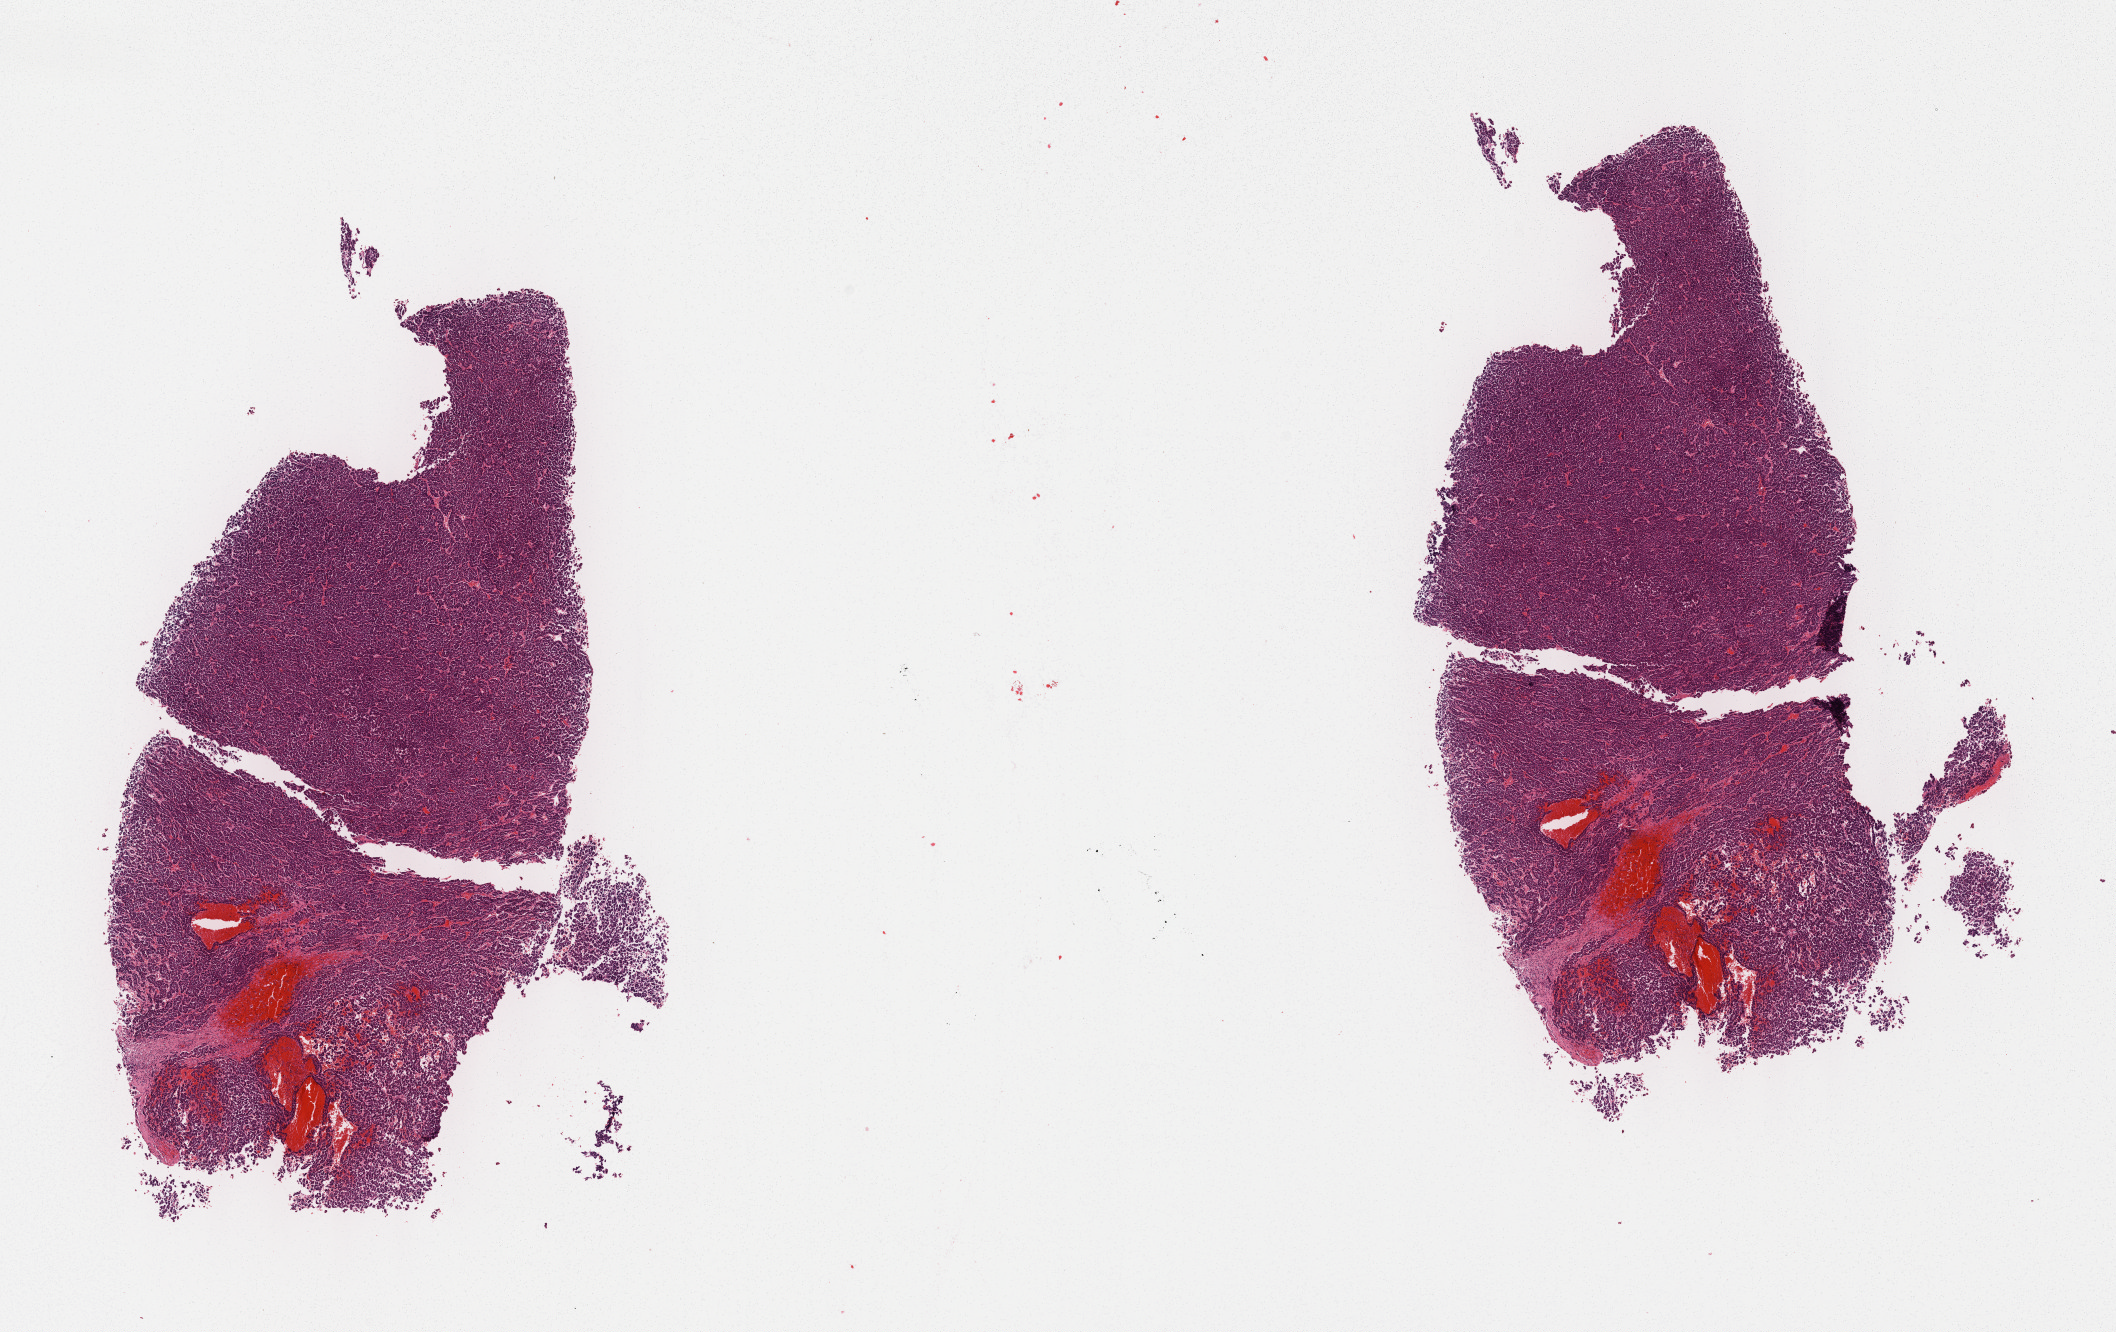
Whole-slide histology image, H&E, a low-resolution overview of the entire scanned area, about 17.1 x 10.8 mm (from a 40x scan); formalin-fixed paraffin-embedded (FFPE) diagnostic section; sample: primary tumour, liver. Patient: male, age at initial diagnosis 50 years. Histologic grade: G3 (poorly differentiated).
AJCC pathologic stage: II. Histologic diagnosis: Hepatocellular carcinoma, NOS. TNM: T2 N0 M0.